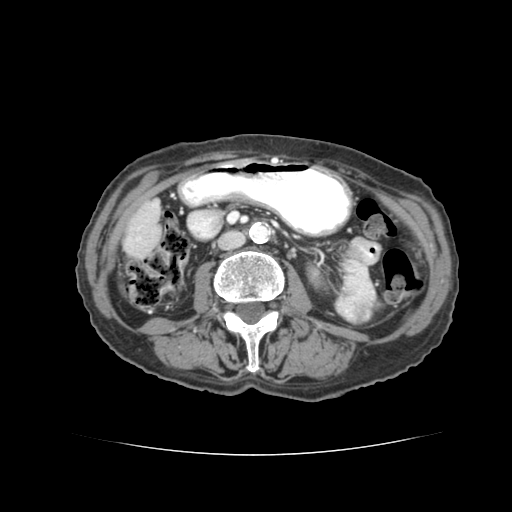
Contrast-enhanced abdominal CT (liver protocol), one axial slice; slice 9 of 77 in the series (ordered by position); 120 kVp; soft-tissue window (W 400 / L 40 HU); 2.5 mm slice thickness; 512 × 512 image matrix, field of view 340 × 340 mm. Case-level facts recorded for this patient, not image findings: diagnosis: hepatocellular carcinoma (patient treated with transarterial chemoembolisation; whether this scan precedes or follows treatment is not stated here); TNM stage (as recorded): Stage-I; Child-Pugh class: A; tumour differentiation: well differentiated; tumour nodularity: uninodular.
Annotated regions visible in this slice (semi-automatic segmentation, software-assisted and operator-edited):
- liver parenchyma outside the tumour (the mass and vessels are separate outlines, so this box may not span the whole liver): bounding box [x1, y1, x2, y2] px = [132, 206, 152, 232]